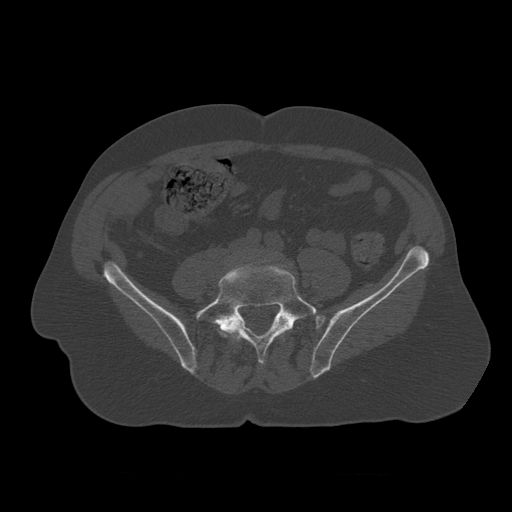
CT including the spine, one axial slice; slice 258 of 450 in the series (ordered by position); reconstruction kernel STANDARD; bone window (W 1800 / L 400 HU); 1.25 mm slice thickness; 512 × 512 image matrix. Patient age 75 years. From the clinical record (not read from this slice): primary cancer: prostate.
Outlined on this slice (semi-automatic segmentation, software-assisted and operator-edited):
- L4 vertebra: bounding box (x1, y1, x2, y2) in pixels: (223, 270, 296, 336)
- L5 vertebra: (195, 265, 318, 364)